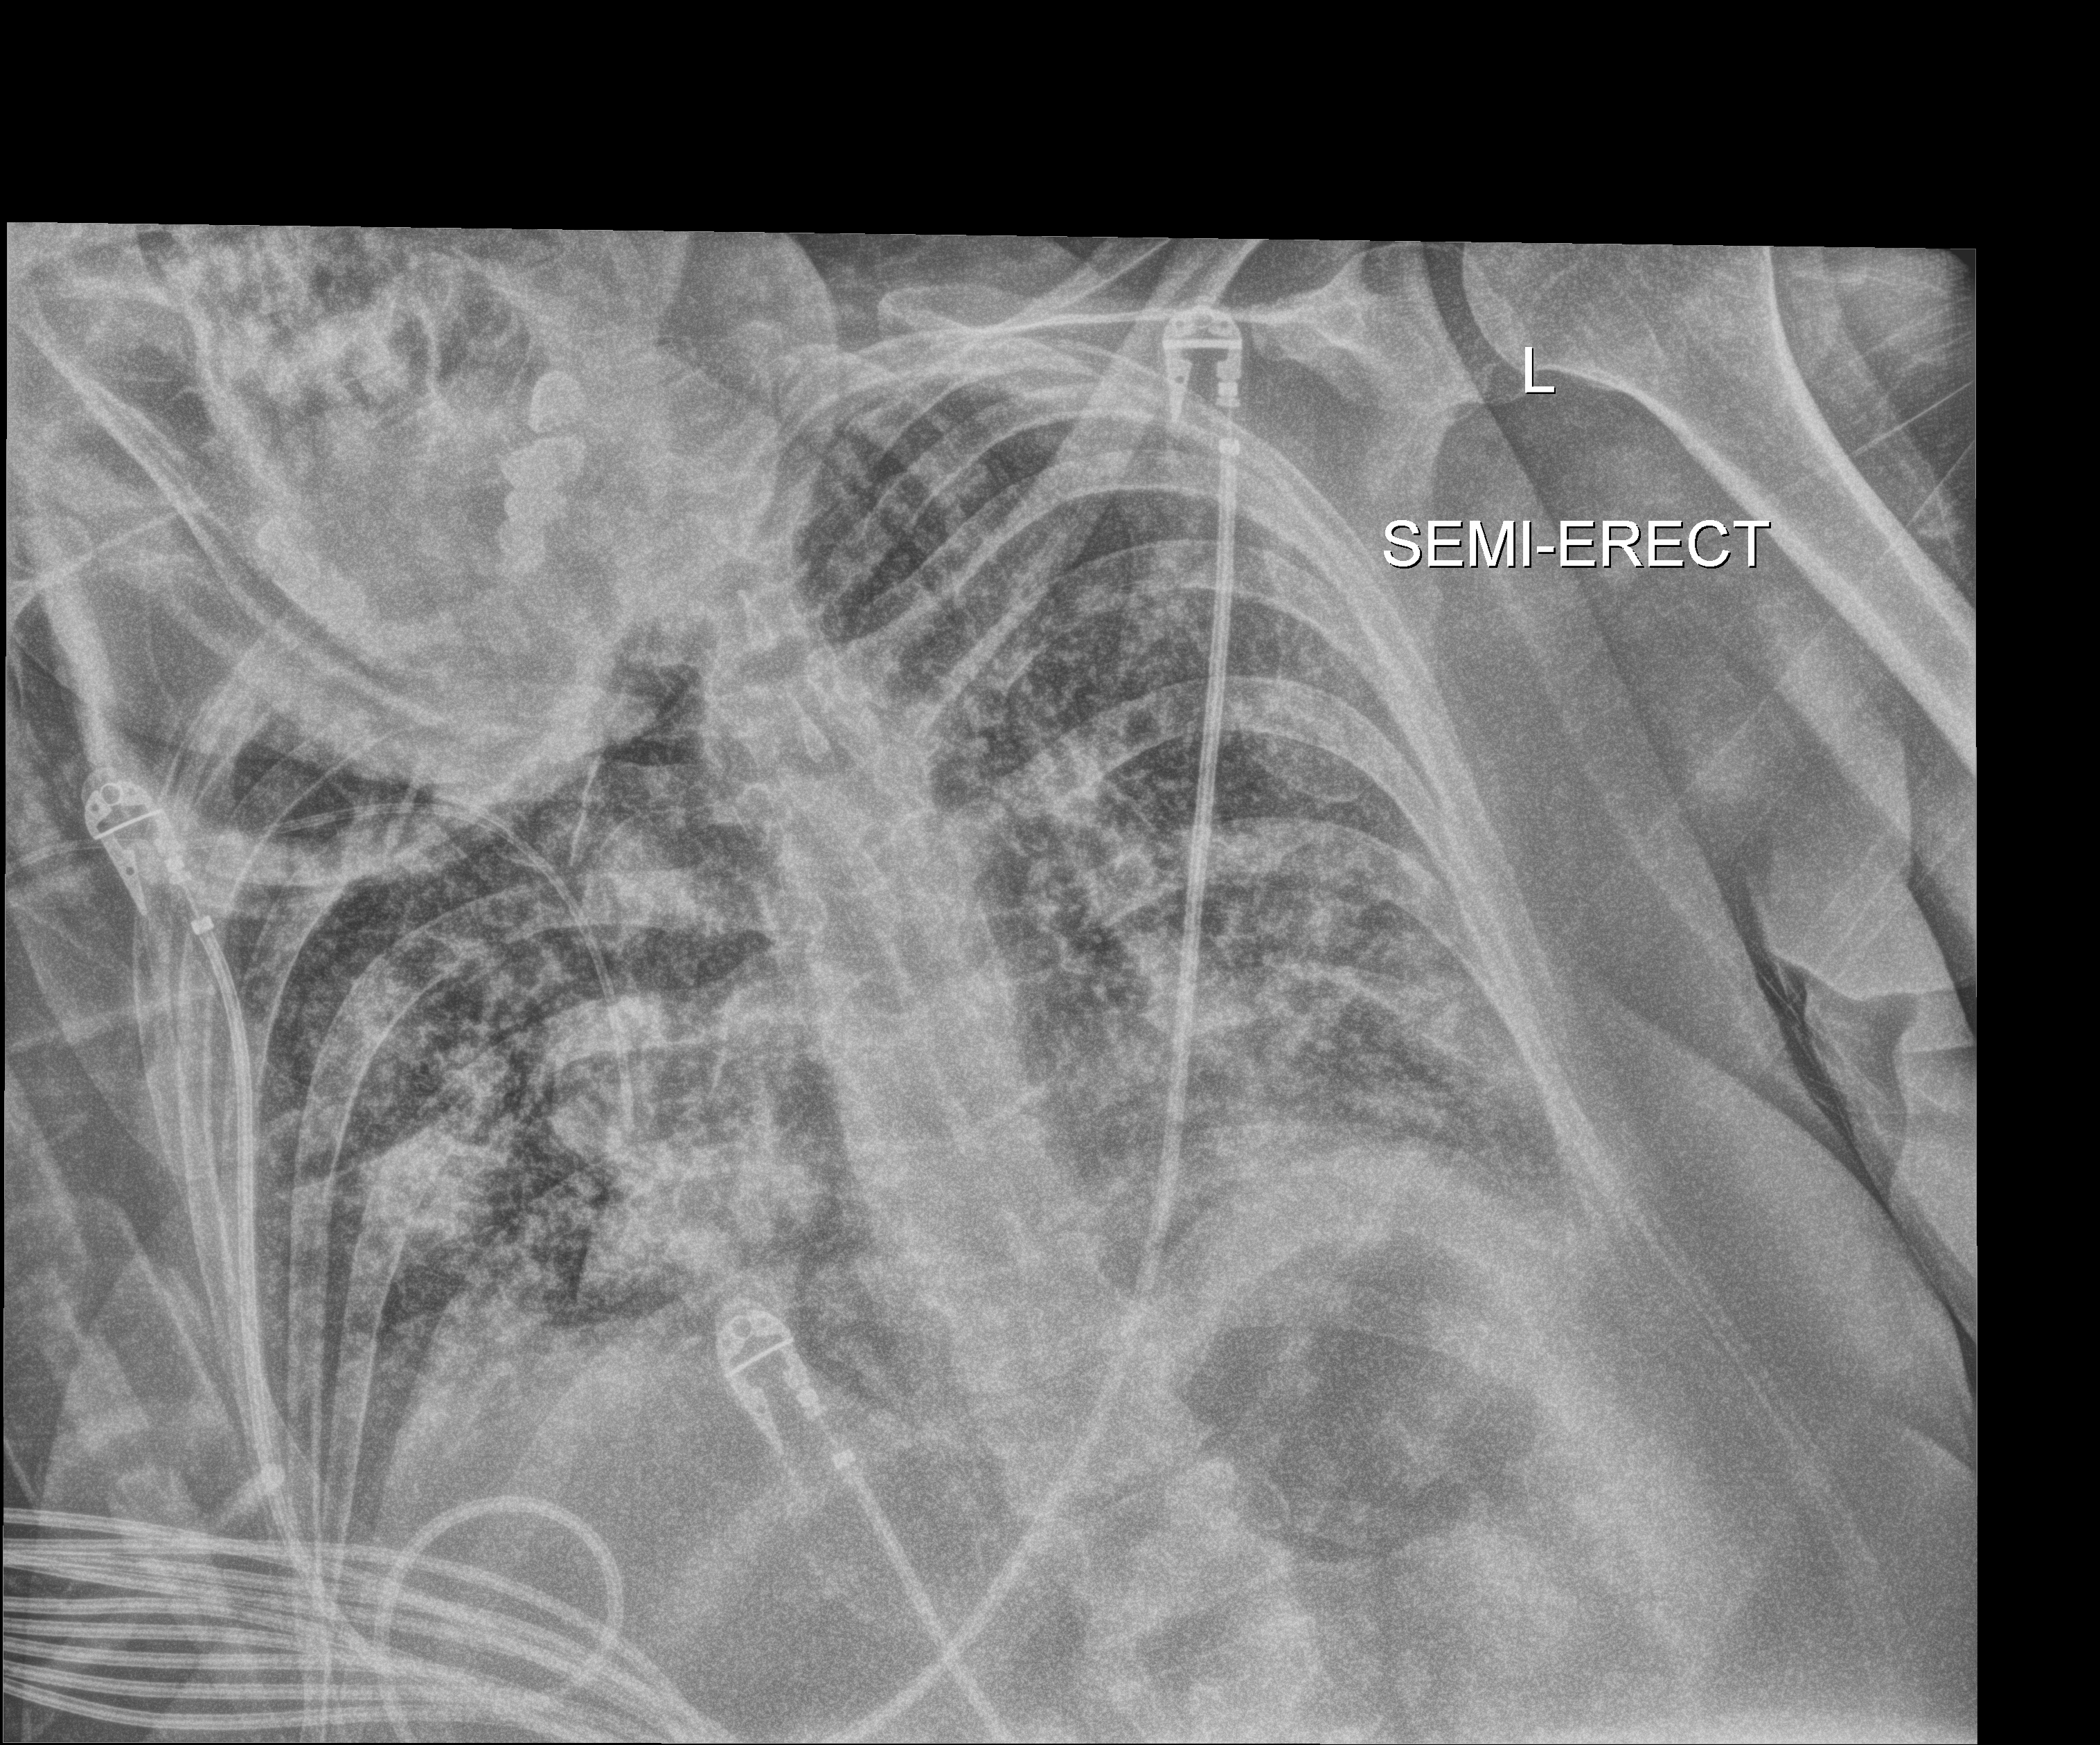
Chest X-ray (portable); anteroposterior (AP) projection. Female patient hospitalised with COVID-19, age 60–74 years.
From the hospital-stay record, not from the radiograph (when in the stay this image was taken is not recorded): length of hospital stay: 45 days; mechanically ventilated during this hospital stay: yes.